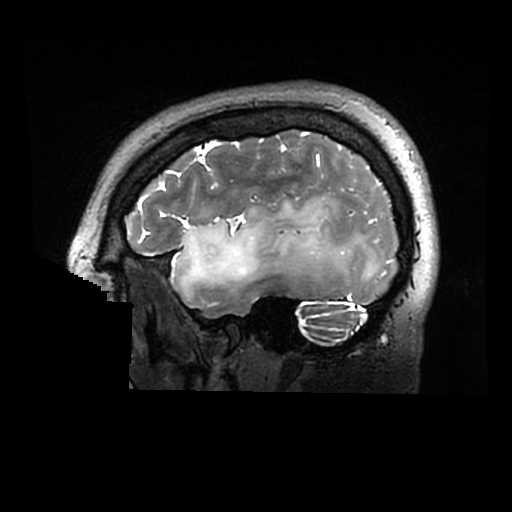
Brain MRI from a brain-tumour surgery series, one sagittal slice; position 232 of 320 along the scan axis; 0.6 mm slice thickness; 512 × 512 image matrix, field of view 240 × 240 mm. Case-level facts recorded for this patient, not image findings: histopathology: Astrocytoma; WHO grade: 2; IDH mutation: yes.
Outlined on this slice (manually delineated by an expert):
- tumour: box from (x=172, y=195) to (x=379, y=297) px